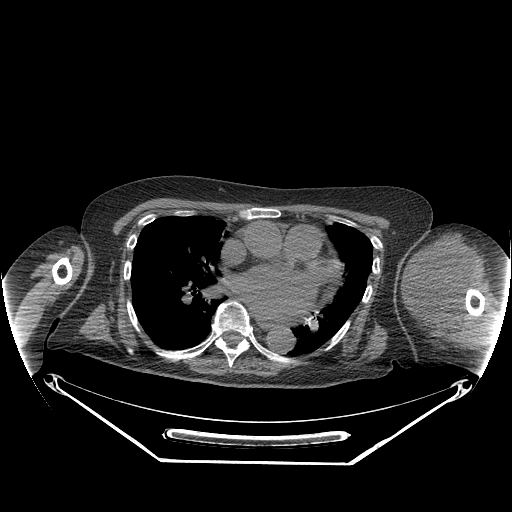
CT of an extremity soft-tissue mass (from a PET/CT study), one axial slice; slice 172 of 267 in the series (ordered by position); reconstruction kernel STANDARD; soft-tissue window (W 400 / L 40 HU); 512 × 512 image matrix, field of view 500 × 500 mm. Female patient. From the clinical record (not read from this slice): histological type: pleiomorphic leiomyosarcoma; grade: high; site of the primary tumour: left biceps.
Structures marked on this image (expert contour drawn on MRI and transferred to this co-registered scan by the dataset authors):
- gross tumour volume including surrounding oedema: bounding box (x1, y1, x2, y2) in pixels: (404, 233, 478, 328)
- gross tumour volume (mass): (404, 233, 474, 321)